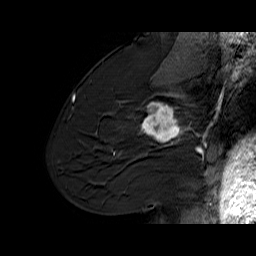
Breast MRI (dynamic contrast-enhanced), one sagittal slice; slice 37 of 60 in the series (ordered by position); dynamic contrast-enhanced series, time point 2 of 6 at this slice position (early post-contrast); 1.5 T; TE 6.1 ms, TR 32.9 ms; 4 mm slice thickness; 256 × 256 image matrix, field of view 220 × 220 mm. Female patient. Case-level facts recorded for this patient, not image findings: setting: breast cancer imaged before/during neoadjuvant chemotherapy; receptor status: HER2-positive.
Outlined on this slice (semi-automatic segmentation, software-assisted and operator-edited):
- analysis volume of interest (the breast-tissue region the enhancement analysis was run in; not a lesion): bounding box <127,95,194,165> (left, top, right, bottom; pixels)
- tumour enhancement mask (voxels above the 100 % enhancement threshold inside the analysis volume of interest): <140,95,190,146>